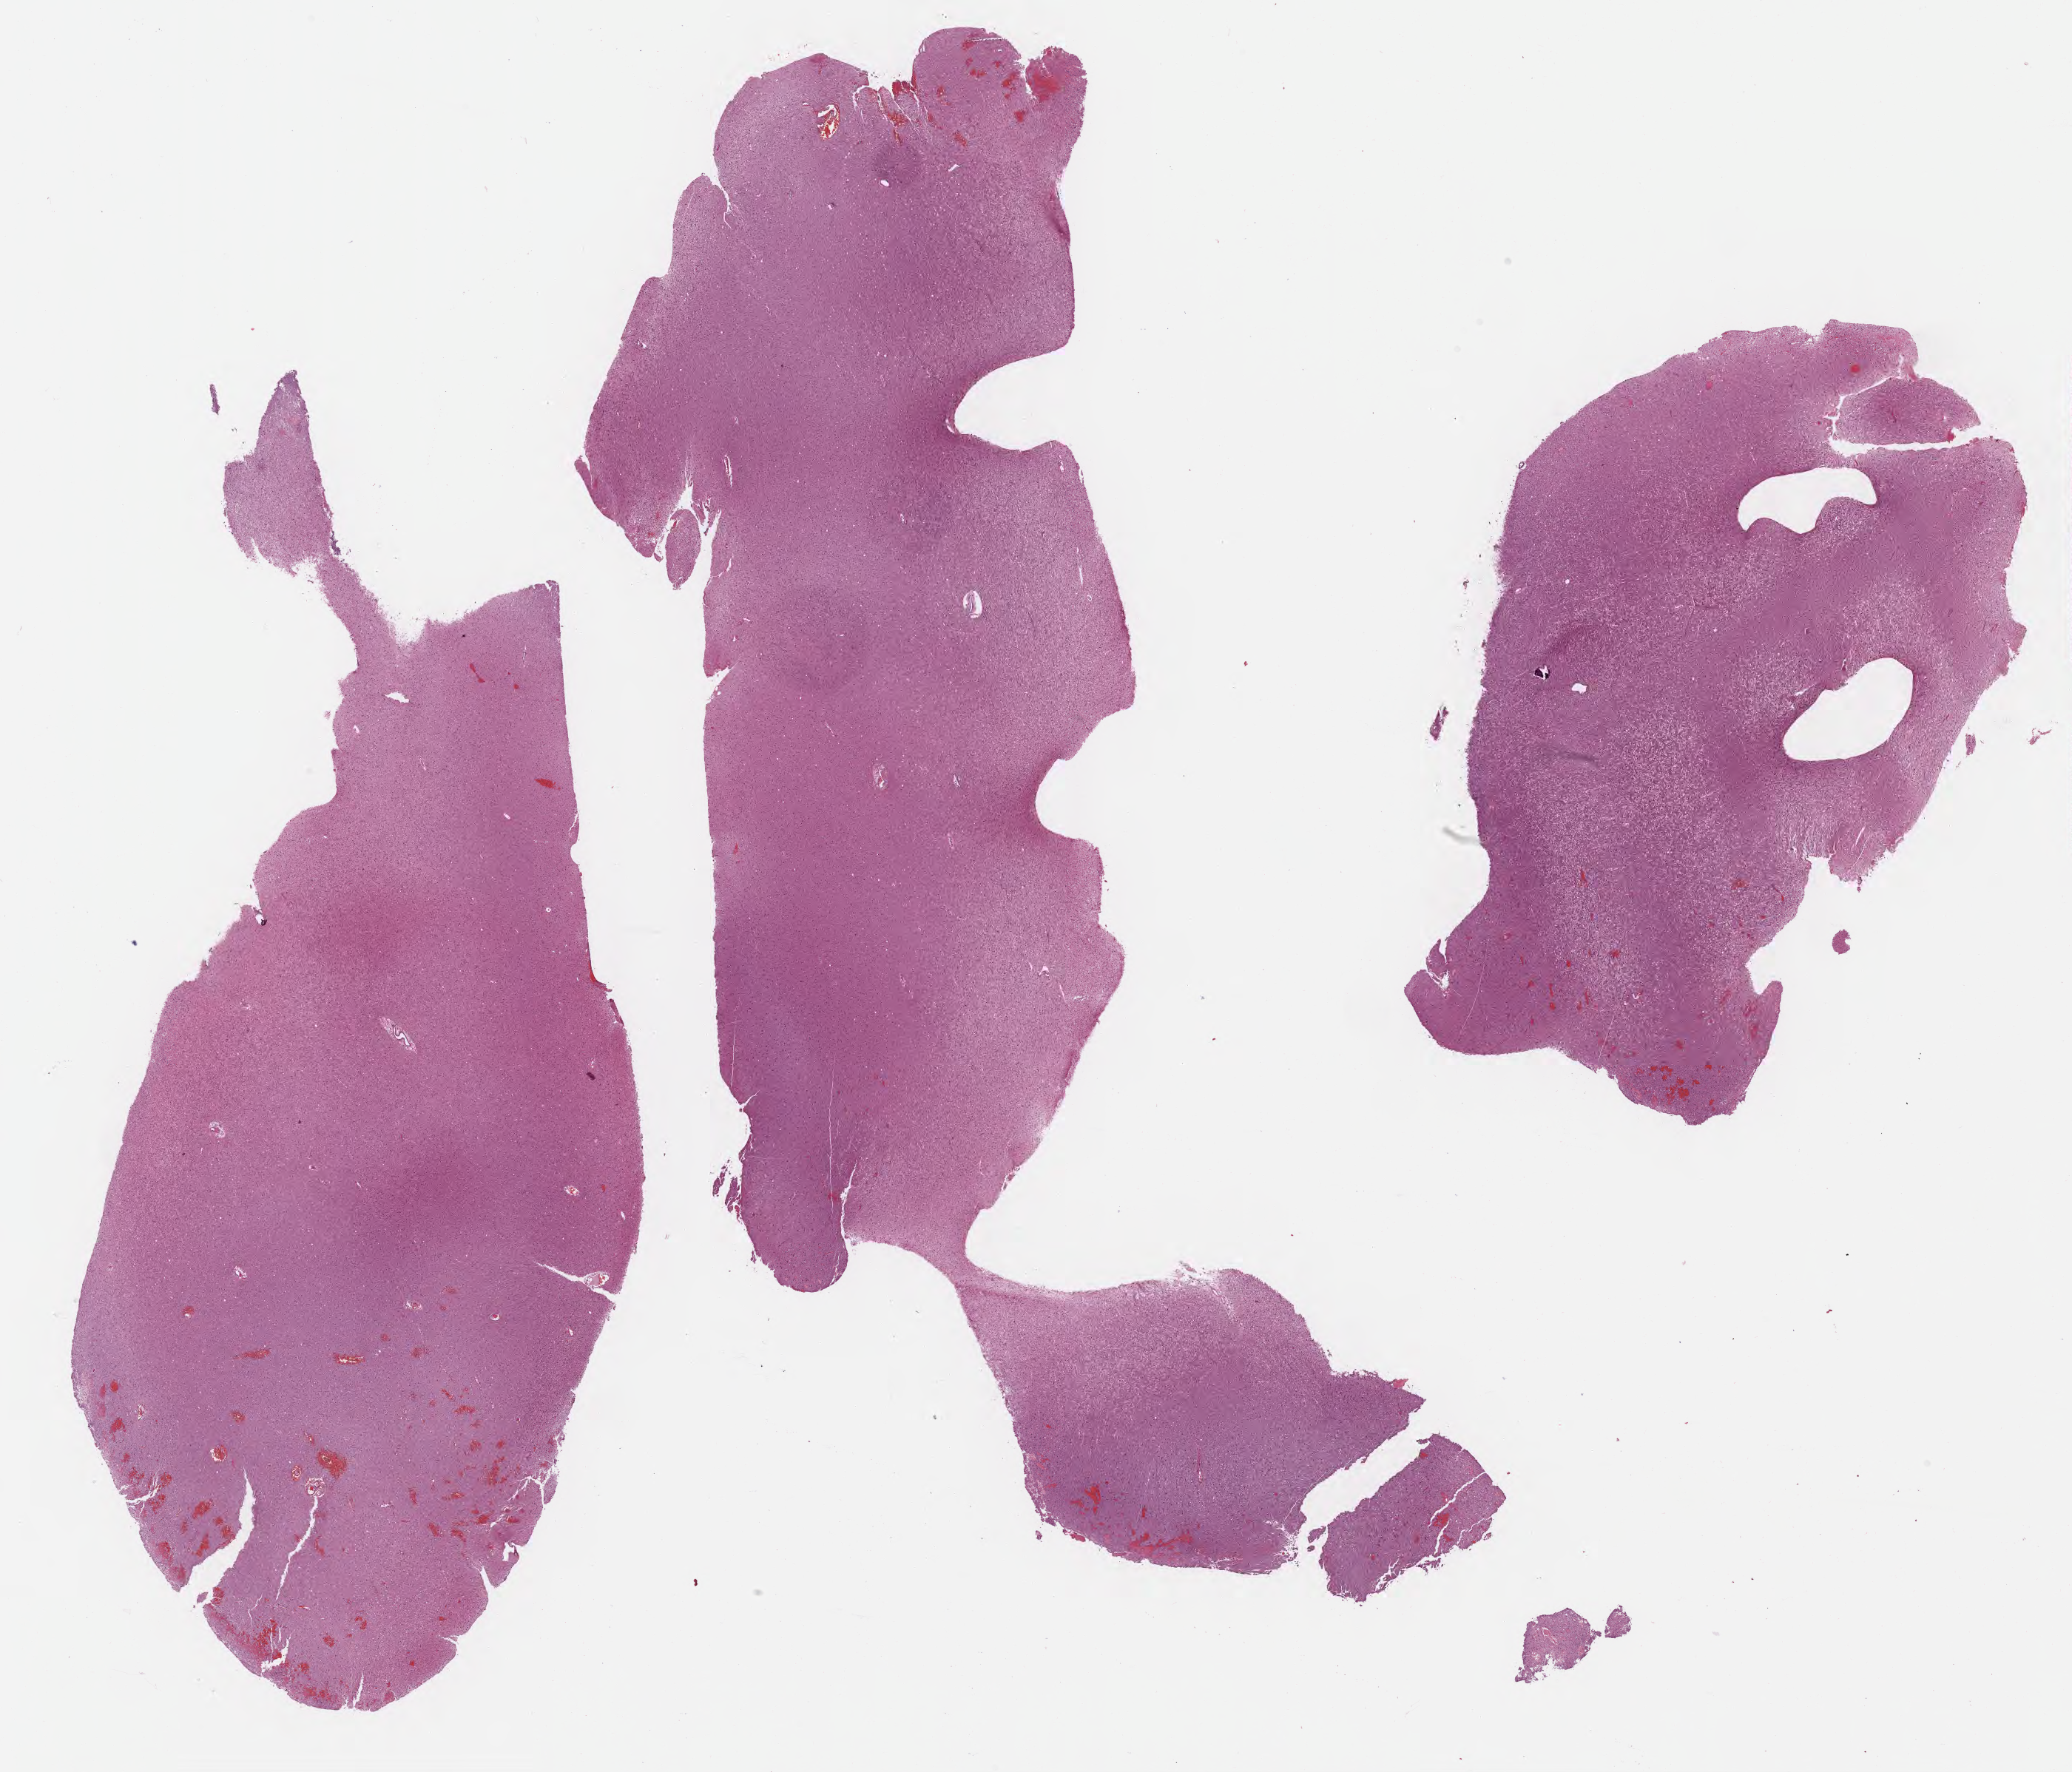
Whole-slide histology image, H&E — low-resolution overview of the scanned area, about 22.7 x 19.4 mm, formalin-fixed paraffin-embedded (FFPE) diagnostic section, brain, primary tumour sample. Patient: male, age at initial diagnosis 38 years.
Pathologic diagnosis: Oligodendroglioma, NOS.